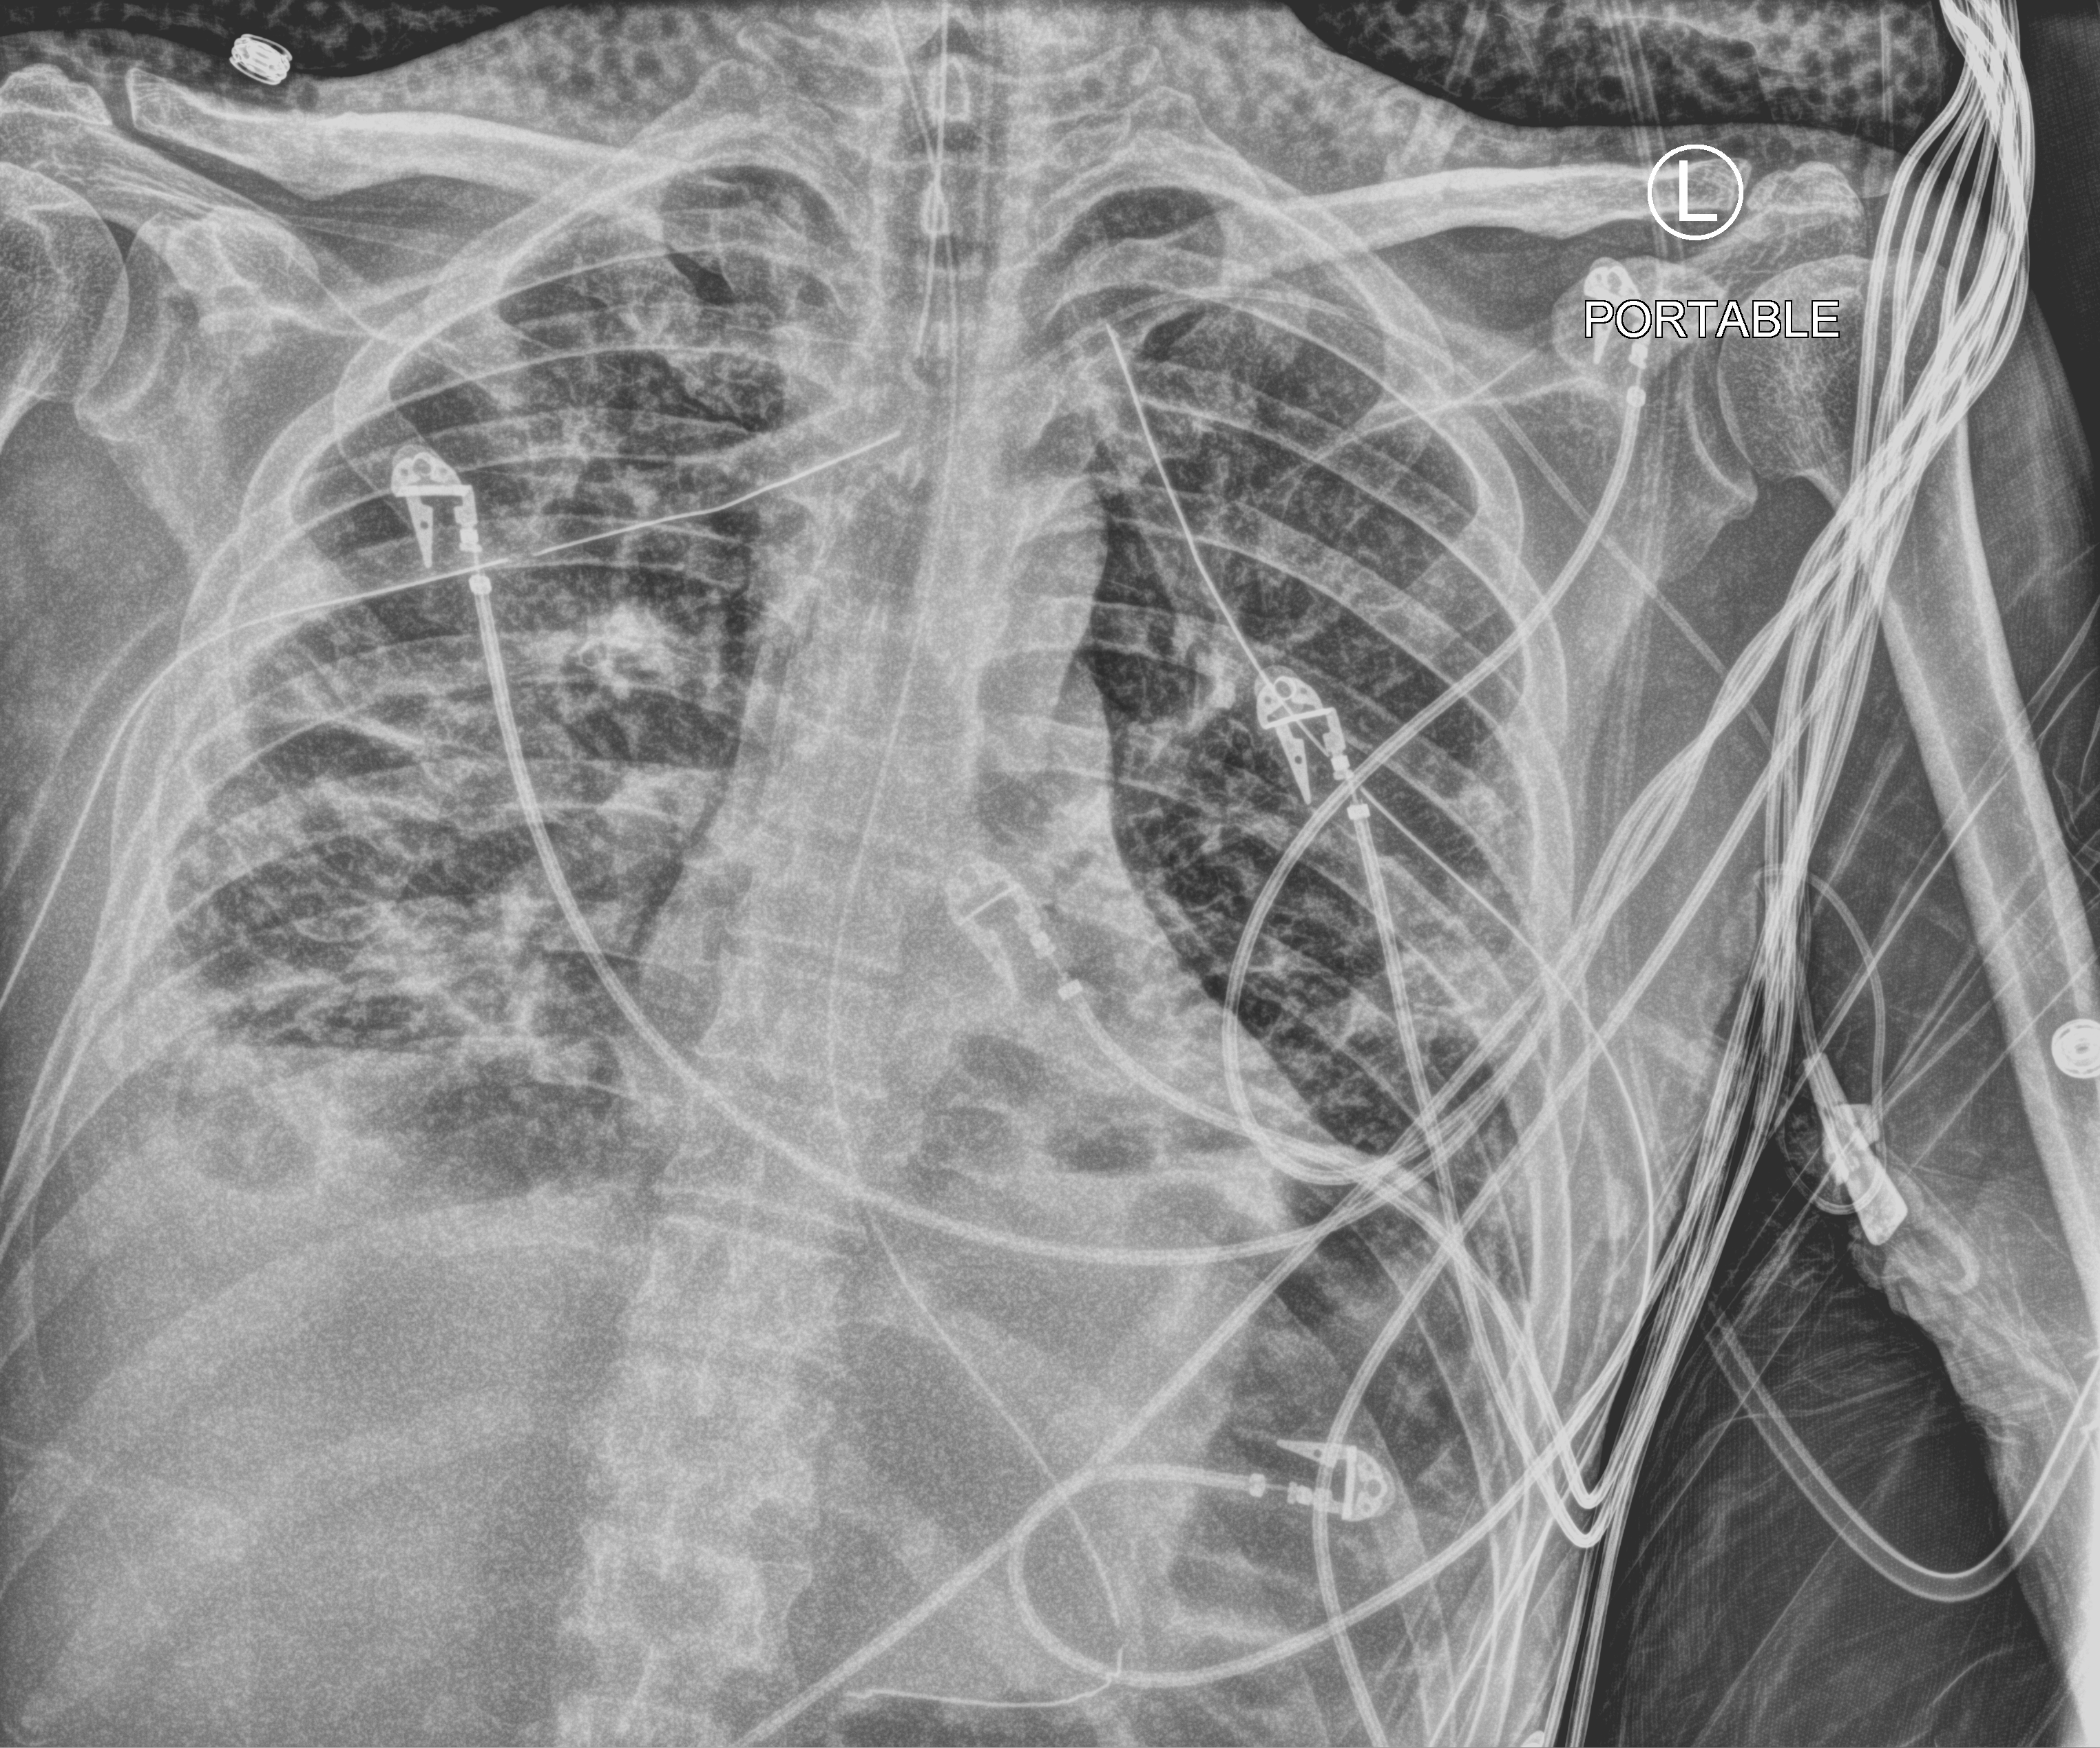
Chest X-ray (portable); anteroposterior (AP) projection. Male patient hospitalised with COVID-19, age 18–59 years.
From the hospital-stay record, not from the radiograph (when in the stay this image was taken is not recorded): COPD (admission record): no.